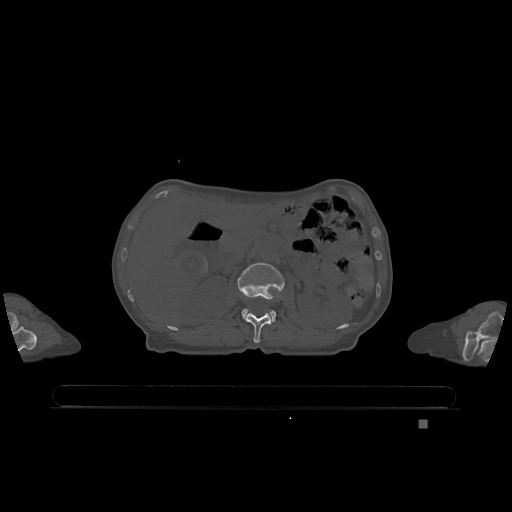
CT including the spine, one axial slice. Slice 449 of 1317 in the series (ordered by position). Bone window (W 1800 / L 400 HU). 512 × 512 image matrix, field of view 500 × 500 mm. Patient: female, 74 years. From the clinical record (not read from this slice): primary cancer: lung; vertebrae with lytic lesions (as recorded): T1, T4, T5, T6, L4, L5.
Outlined on this slice (semi-automatic segmentation, software-assisted and operator-edited):
- L1 vertebra: bounding box [x1, y1, x2, y2] px = [244, 313, 271, 343]
- L2 vertebra: [238, 263, 285, 322]